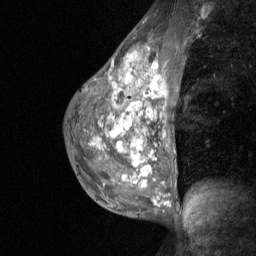
Breast MRI (dynamic contrast-enhanced), one sagittal slice. Slice 37 of 64 in the series (ordered by position). Dynamic contrast-enhanced study with each time point stored as its own series, time point 2 of 3 at this slice position (early post-contrast, ordered by acquisition time). 1.5 T. TE 4.8 ms, TR 27 ms. 2 mm slice thickness. 256 × 256 image matrix, field of view 200 × 200 mm. Female patient, age 36 years. From the clinical record (not read from this slice): setting: breast cancer imaged before/during neoadjuvant chemotherapy; receptor status: HR-positive, HER2-negative.
Outlined on this slice (semi-automatically segmented with operator editing):
- analysis volume of interest (the breast-tissue region the enhancement analysis was run in; not a lesion): box from (x=73, y=48) to (x=181, y=210) px
- tumour enhancement mask (voxels above the 90 % enhancement threshold inside the analysis volume of interest): (x=96, y=86)–(x=157, y=203)